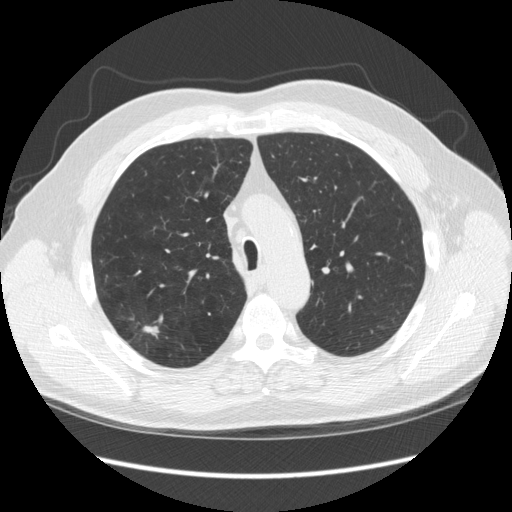
Low-dose screening chest CT, one axial slice; slice 181 of 248 in the series (ordered by position); reconstruction kernel STANDARD; lung window (W 1500 / L -600 HU); 2.5 mm slice thickness; 512 × 512 image matrix.
Outlined on this slice (outlined manually by an expert reader):
- lesion 1 (tumor, upper lobe of right lung): bounding box [x1, y1, x2, y2] px = [143, 325, 160, 335]